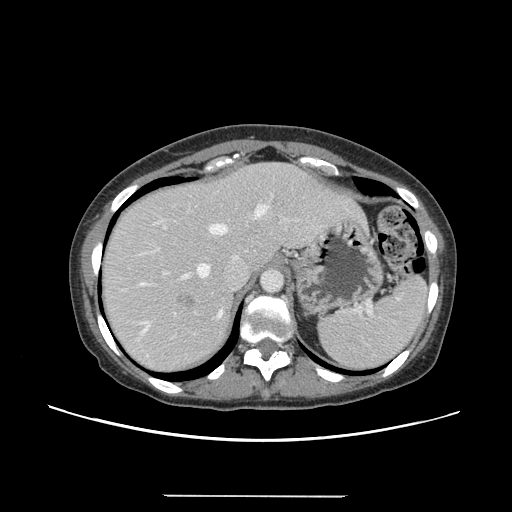
Contrast-enhanced abdominal CT, one axial slice. Slice 112 of 144 in the series (ordered by position). 120 kVp. Intravenous contrast given. Soft-tissue window (W 400 / L 40 HU). 2.5 mm slice thickness. 512 × 512 image matrix, field of view 380 × 380 mm. Female patient, age 53 years. Case-level facts recorded for this patient, not image findings: diagnosis: colorectal cancer liver metastases, imaged before liver resection; multiple liver metastases: yes; largest metastasis: 1.1 cm; disease in both lobes: no.
Annotated regions visible in this slice (manually delineated by an expert):
- hepatic veins: bounding box (x1, y1, x2, y2) in pixels: (141, 206, 267, 333)
- liver: (102, 163, 362, 372)
- planned liver remnant (the part of the liver to remain after resection): (101, 163, 293, 301)
- portal vein (with intrahepatic branches): (153, 219, 286, 275)
- liver metastasis: (177, 295, 194, 307)
- liver metastasis: (166, 355, 172, 360)